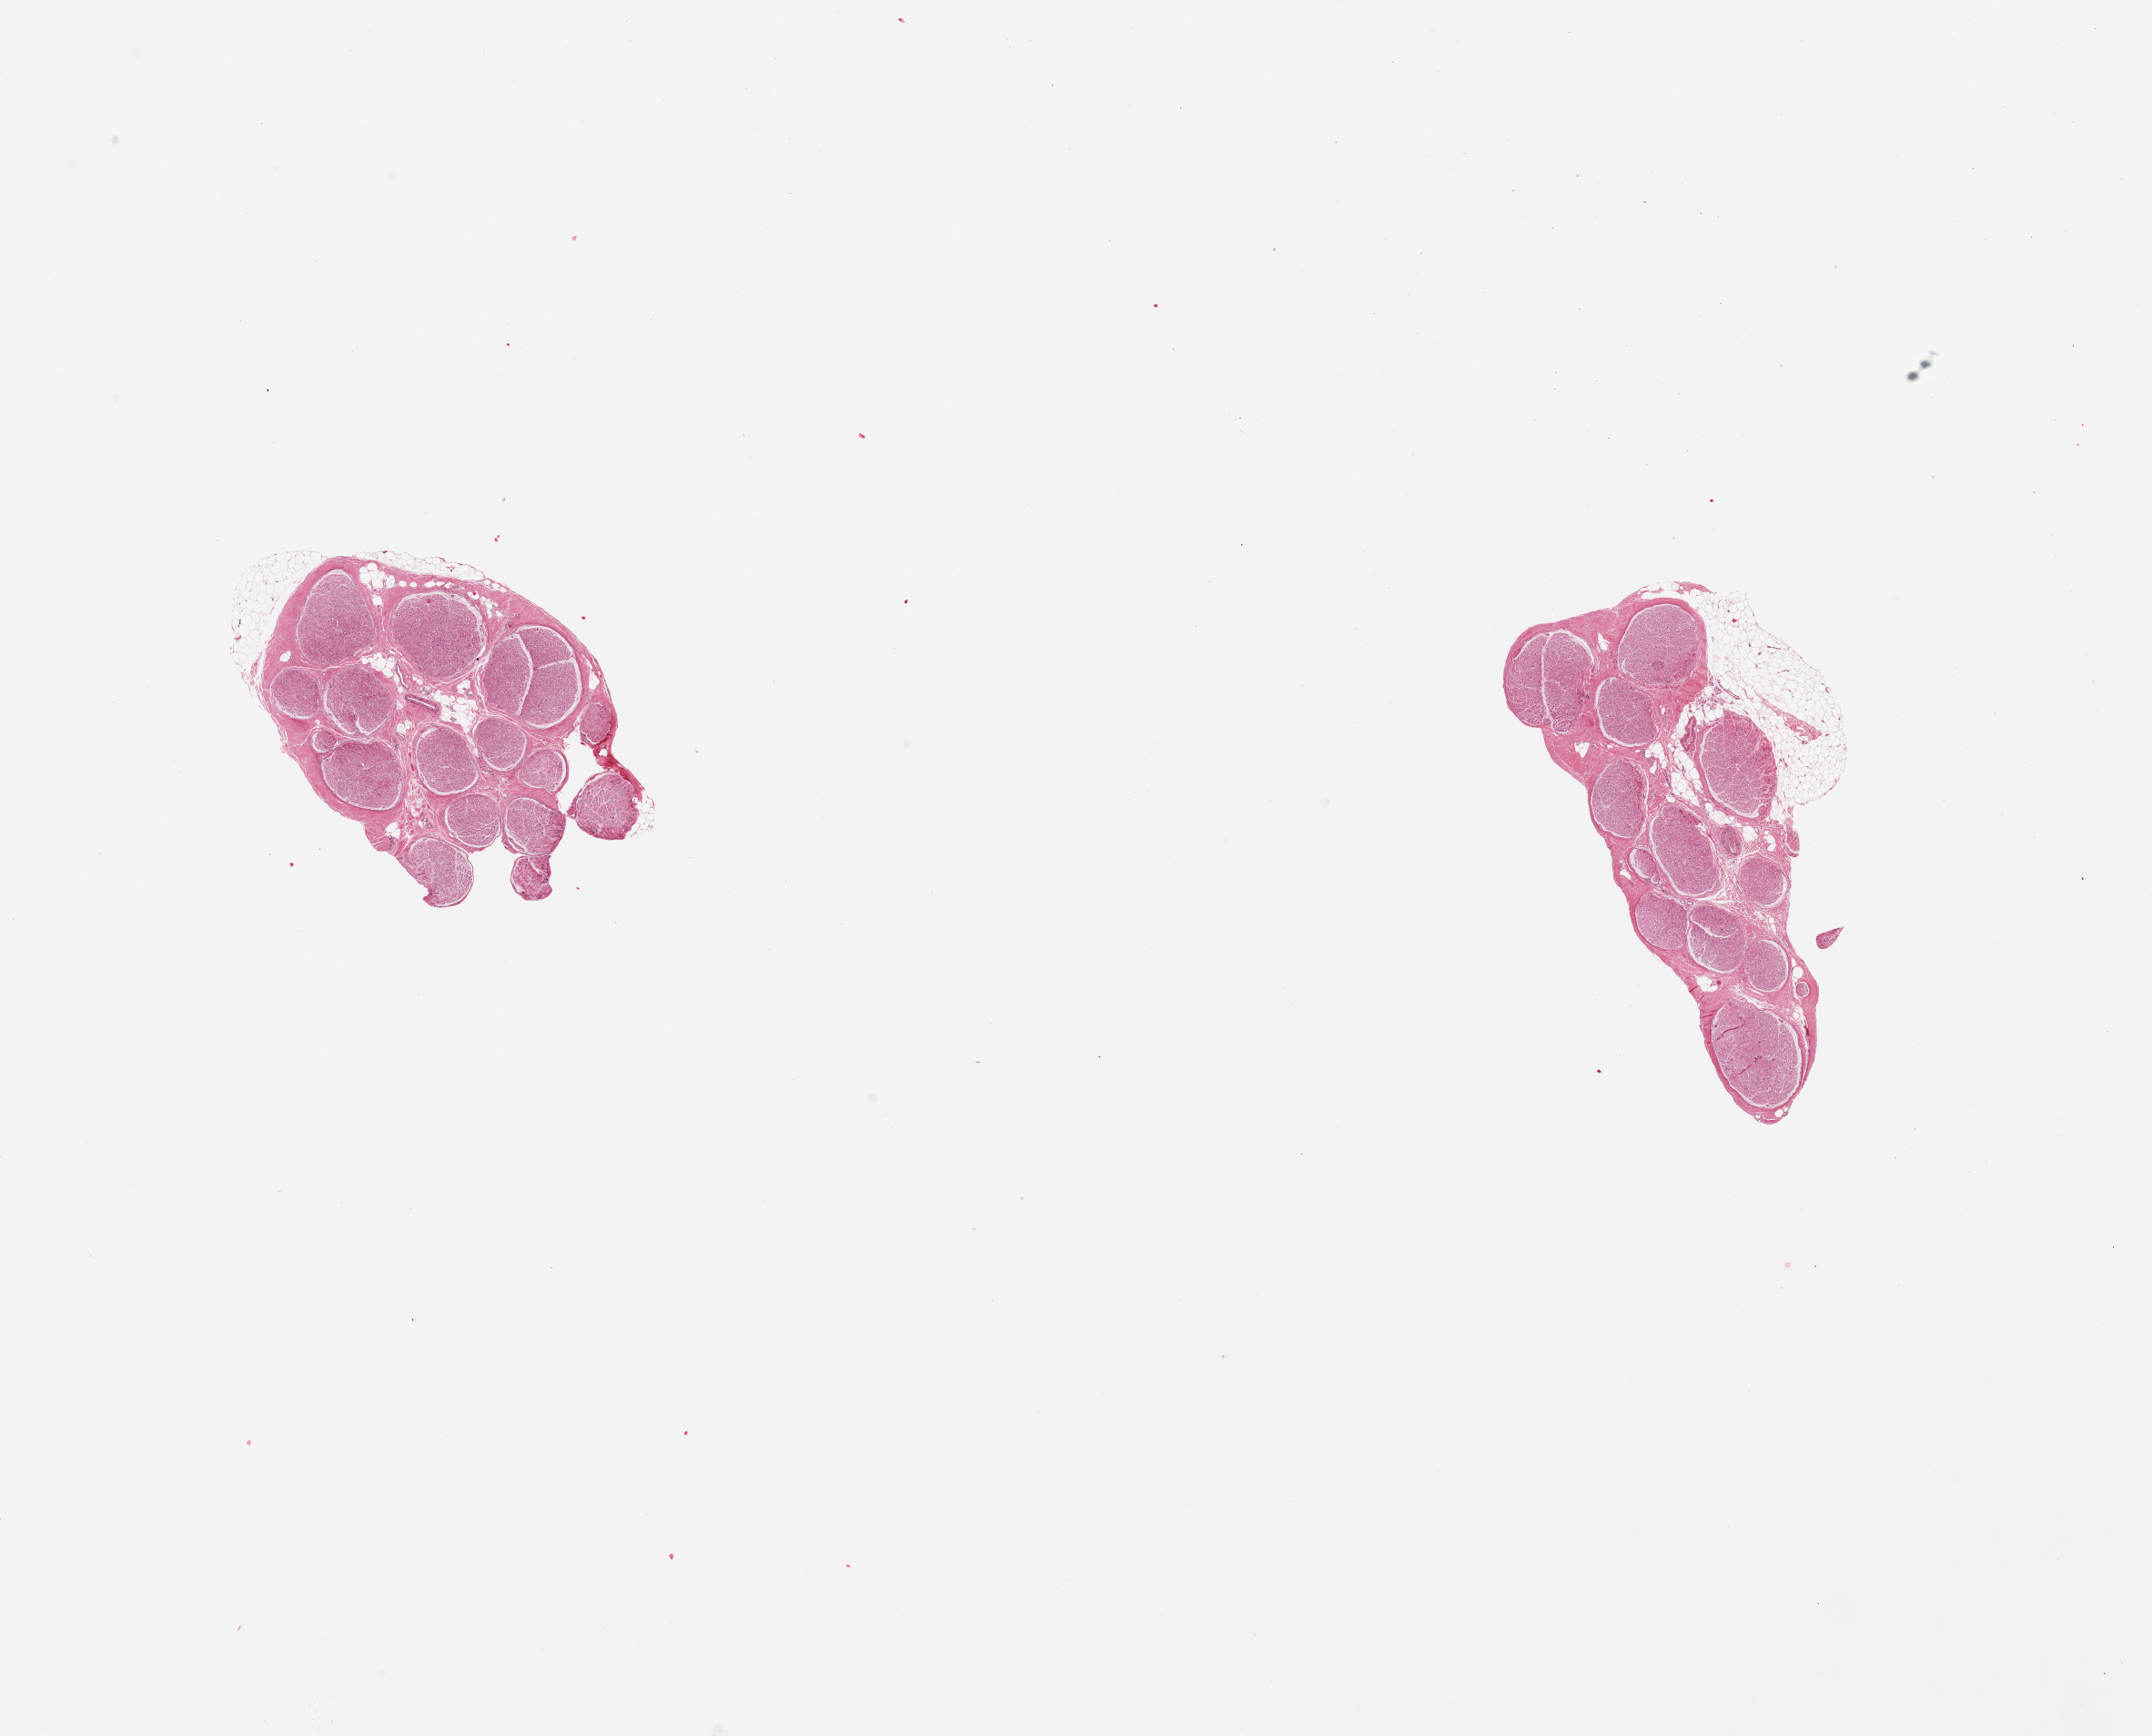
Digitized haematoxylin and eosin-stained section, whole scanned area (about 18.7 x 15.1 mm) shown as a low-resolution overview, PAXgene-fixed, paraffin-embedded tissue, section of tibial nerve (target tissue), donor tissue sample. Donor sex: female.
• review note (as recorded): 2 pieces; 20% & 10% internal & external fat